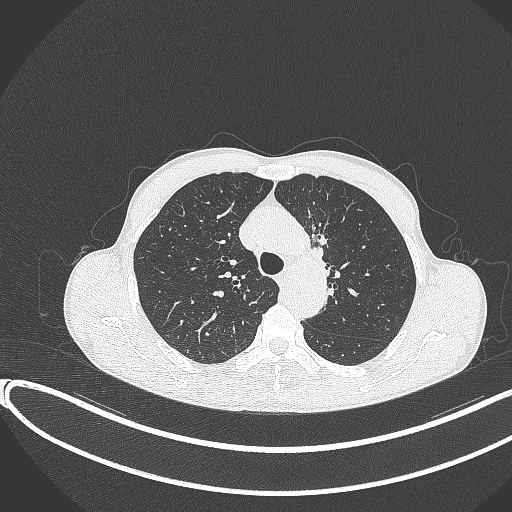
Chest CT, one axial slice; position 271 of 374 along the scan axis; 120 kVp; lung window (W 1500 / L -600 HU); 1 mm slice thickness; 512 × 512 image matrix. Male patient, age 58 years. Case-level facts recorded for this patient, not image findings: clinical TNM (as recorded): T1c N1 M0.
Structures marked on this image (bounding box drawn by a radiologist):
- lung tumour (recorded histology: adenocarcinoma): bounding box <306,216,331,269> (left, top, right, bottom; pixels)